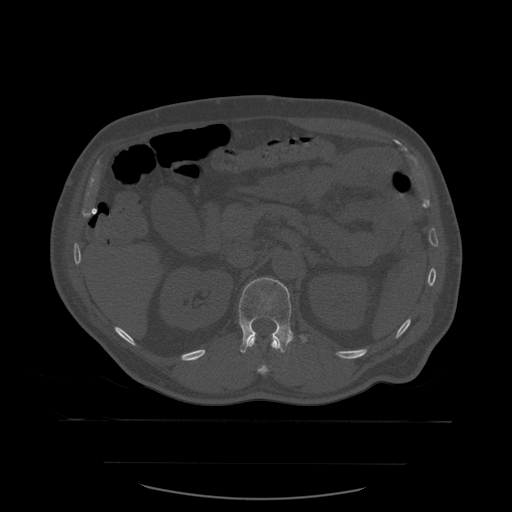
CT including the spine, one axial slice; position 253 of 590 along the scan axis; bone window (W 1800 / L 400 HU); 512 × 512 image matrix. Patient age 71 years. From the clinical record (not read from this slice): primary cancer: lung.
Structures marked on this image (semi-automatically segmented with operator editing):
- L1 vertebra: bounding box <239,278,307,354> (left, top, right, bottom; pixels)
- T12 vertebra: <241,337,286,375>